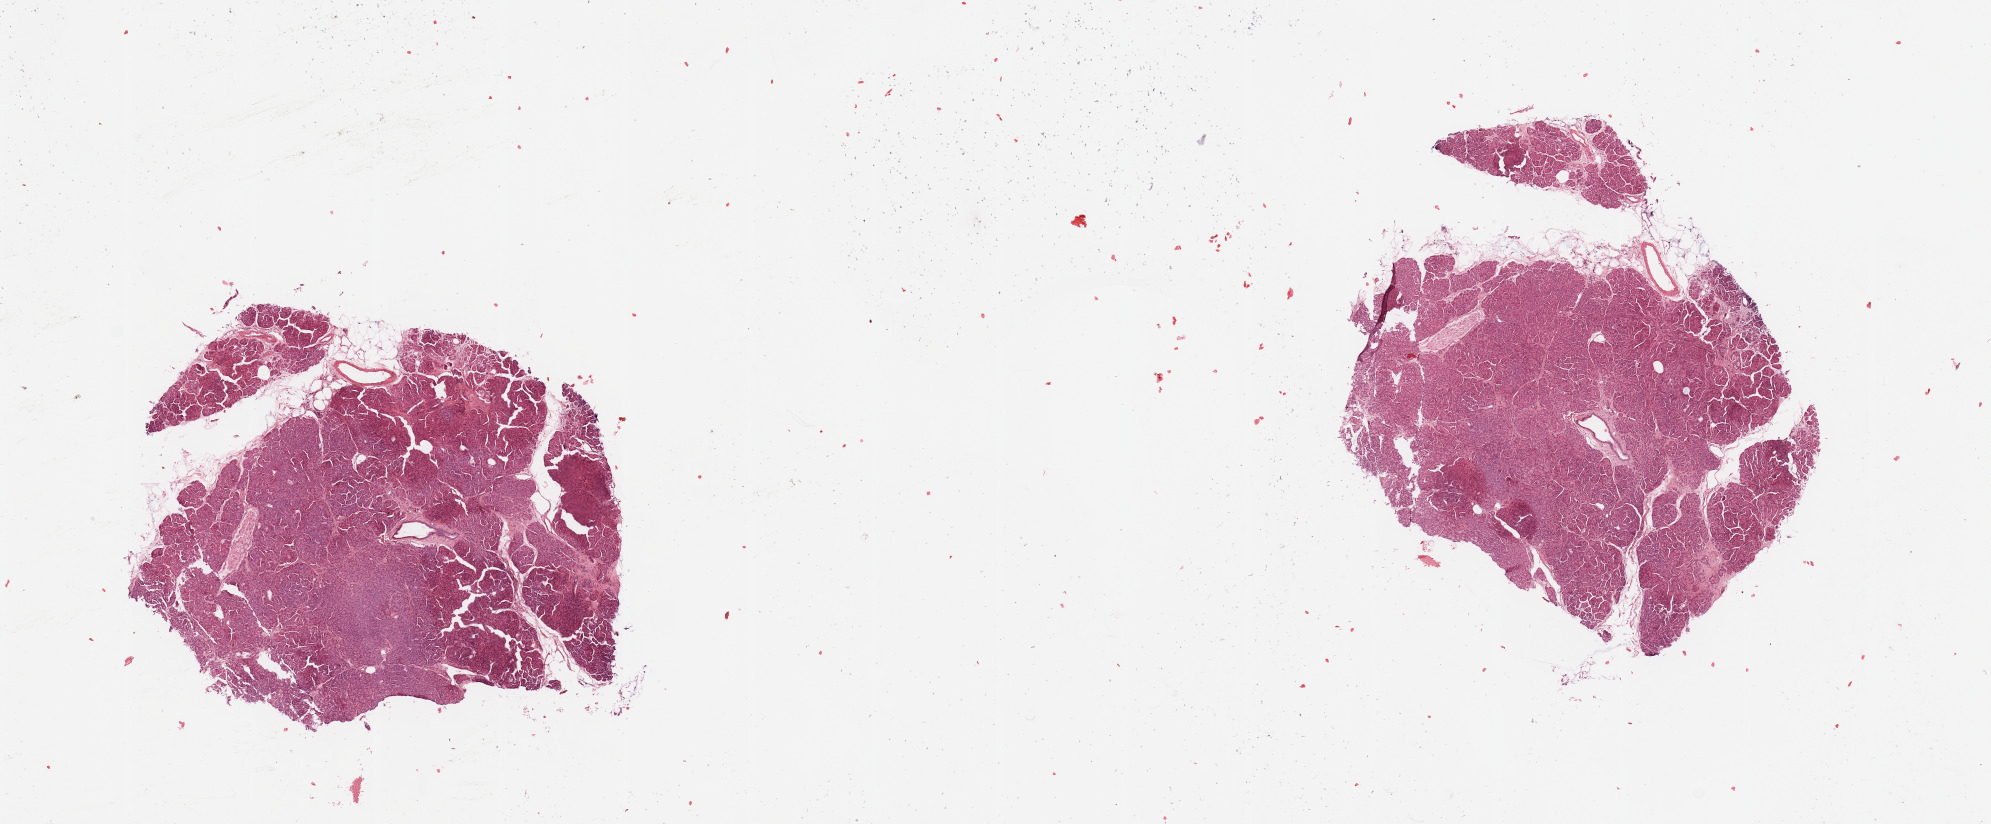
Digitized H&E-stained tissue section (whole slide) — shown as a low-resolution overview of the whole scanned area (about 15.8 x 6.5 mm). Normal (non-tumour) tissue sample, sampled site: pancreas. Male, 42 y/o.
This section: normal (non-tumour) tissue from the same patient. Patient diagnosis: Infiltrating duct carcinoma, NOS.